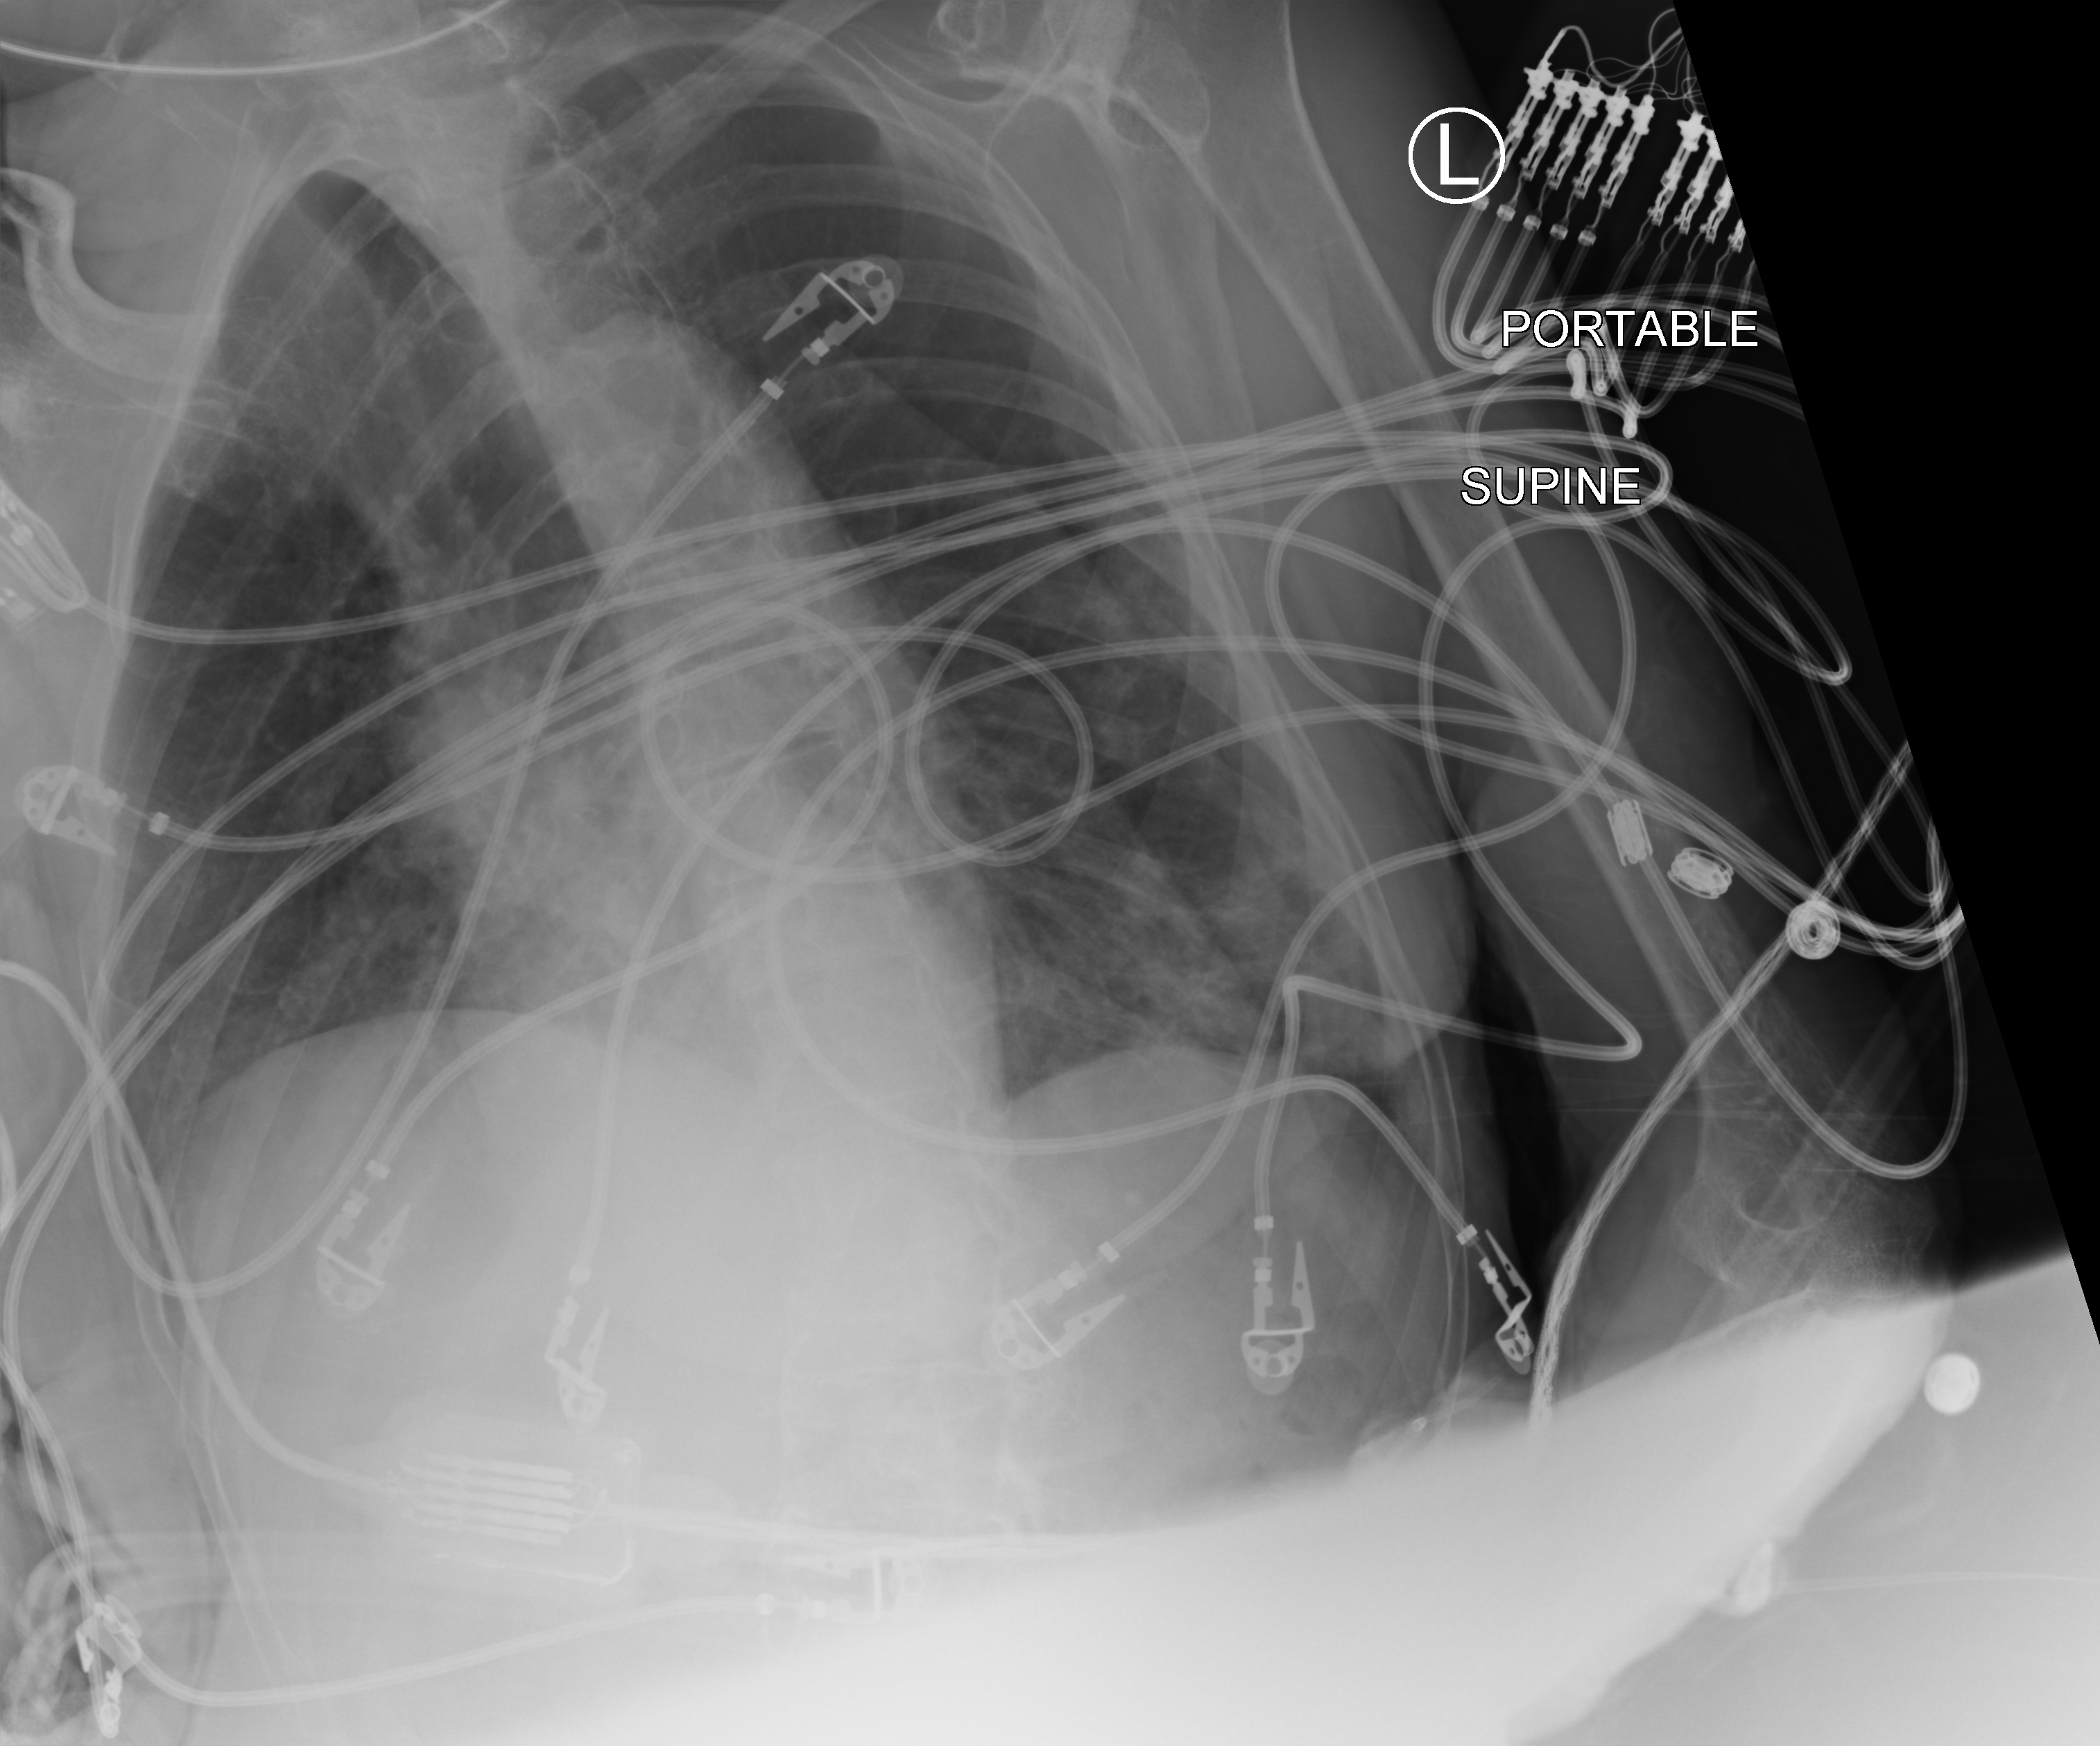
Chest X-ray (portable). Patient hospitalised with COVID-19; female, aged 75–90 years.
Admission-level facts for this patient (not findings on this image; timing relative to this image not recorded): admitted to intensive care during this hospital stay: yes.